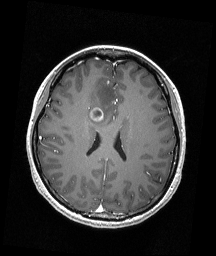
Brain MRI from a brain-tumour surgery series, one axial slice. Slice 76 of 192 in the series (ordered by position). T1-weighted post-contrast. 216 × 256 image matrix, field of view 211 × 250 mm. Case-level facts recorded for this patient, not image findings: histopathology: Astrocytoma; WHO grade: 4; IDH mutation: yes.
Outlined on this slice (expert manual segmentation):
- tumour: bounding box (x1, y1, x2, y2) in pixels: (90, 108, 103, 121)